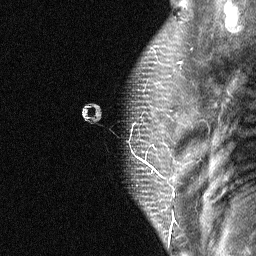
Breast MRI (dynamic contrast-enhanced), one sagittal slice; slice 52 of 64 in the series (ordered by position); dynamic contrast-enhanced study with each time point stored as its own series, time point 2 of 4 at this slice position (early post-contrast, ordered by acquisition time); 1.5 T; TE 4.8 ms, TR 27 ms; 2 mm slice thickness; 256 × 256 image matrix, field of view 180 × 180 mm. Patient: female, 50 years. Case-level facts recorded for this patient, not image findings: setting: breast cancer imaged before/during neoadjuvant chemotherapy; receptor status: HER2-positive.
Outlined on this slice (semi-automatic segmentation, software-assisted and operator-edited):
- analysis volume of interest (the breast-tissue region the enhancement analysis was run in; not a lesion): bounding box [x1, y1, x2, y2] px = [125, 91, 189, 177]
- tumour enhancement mask (voxels above the 90 % enhancement threshold inside the analysis volume of interest): [151, 167, 155, 172]